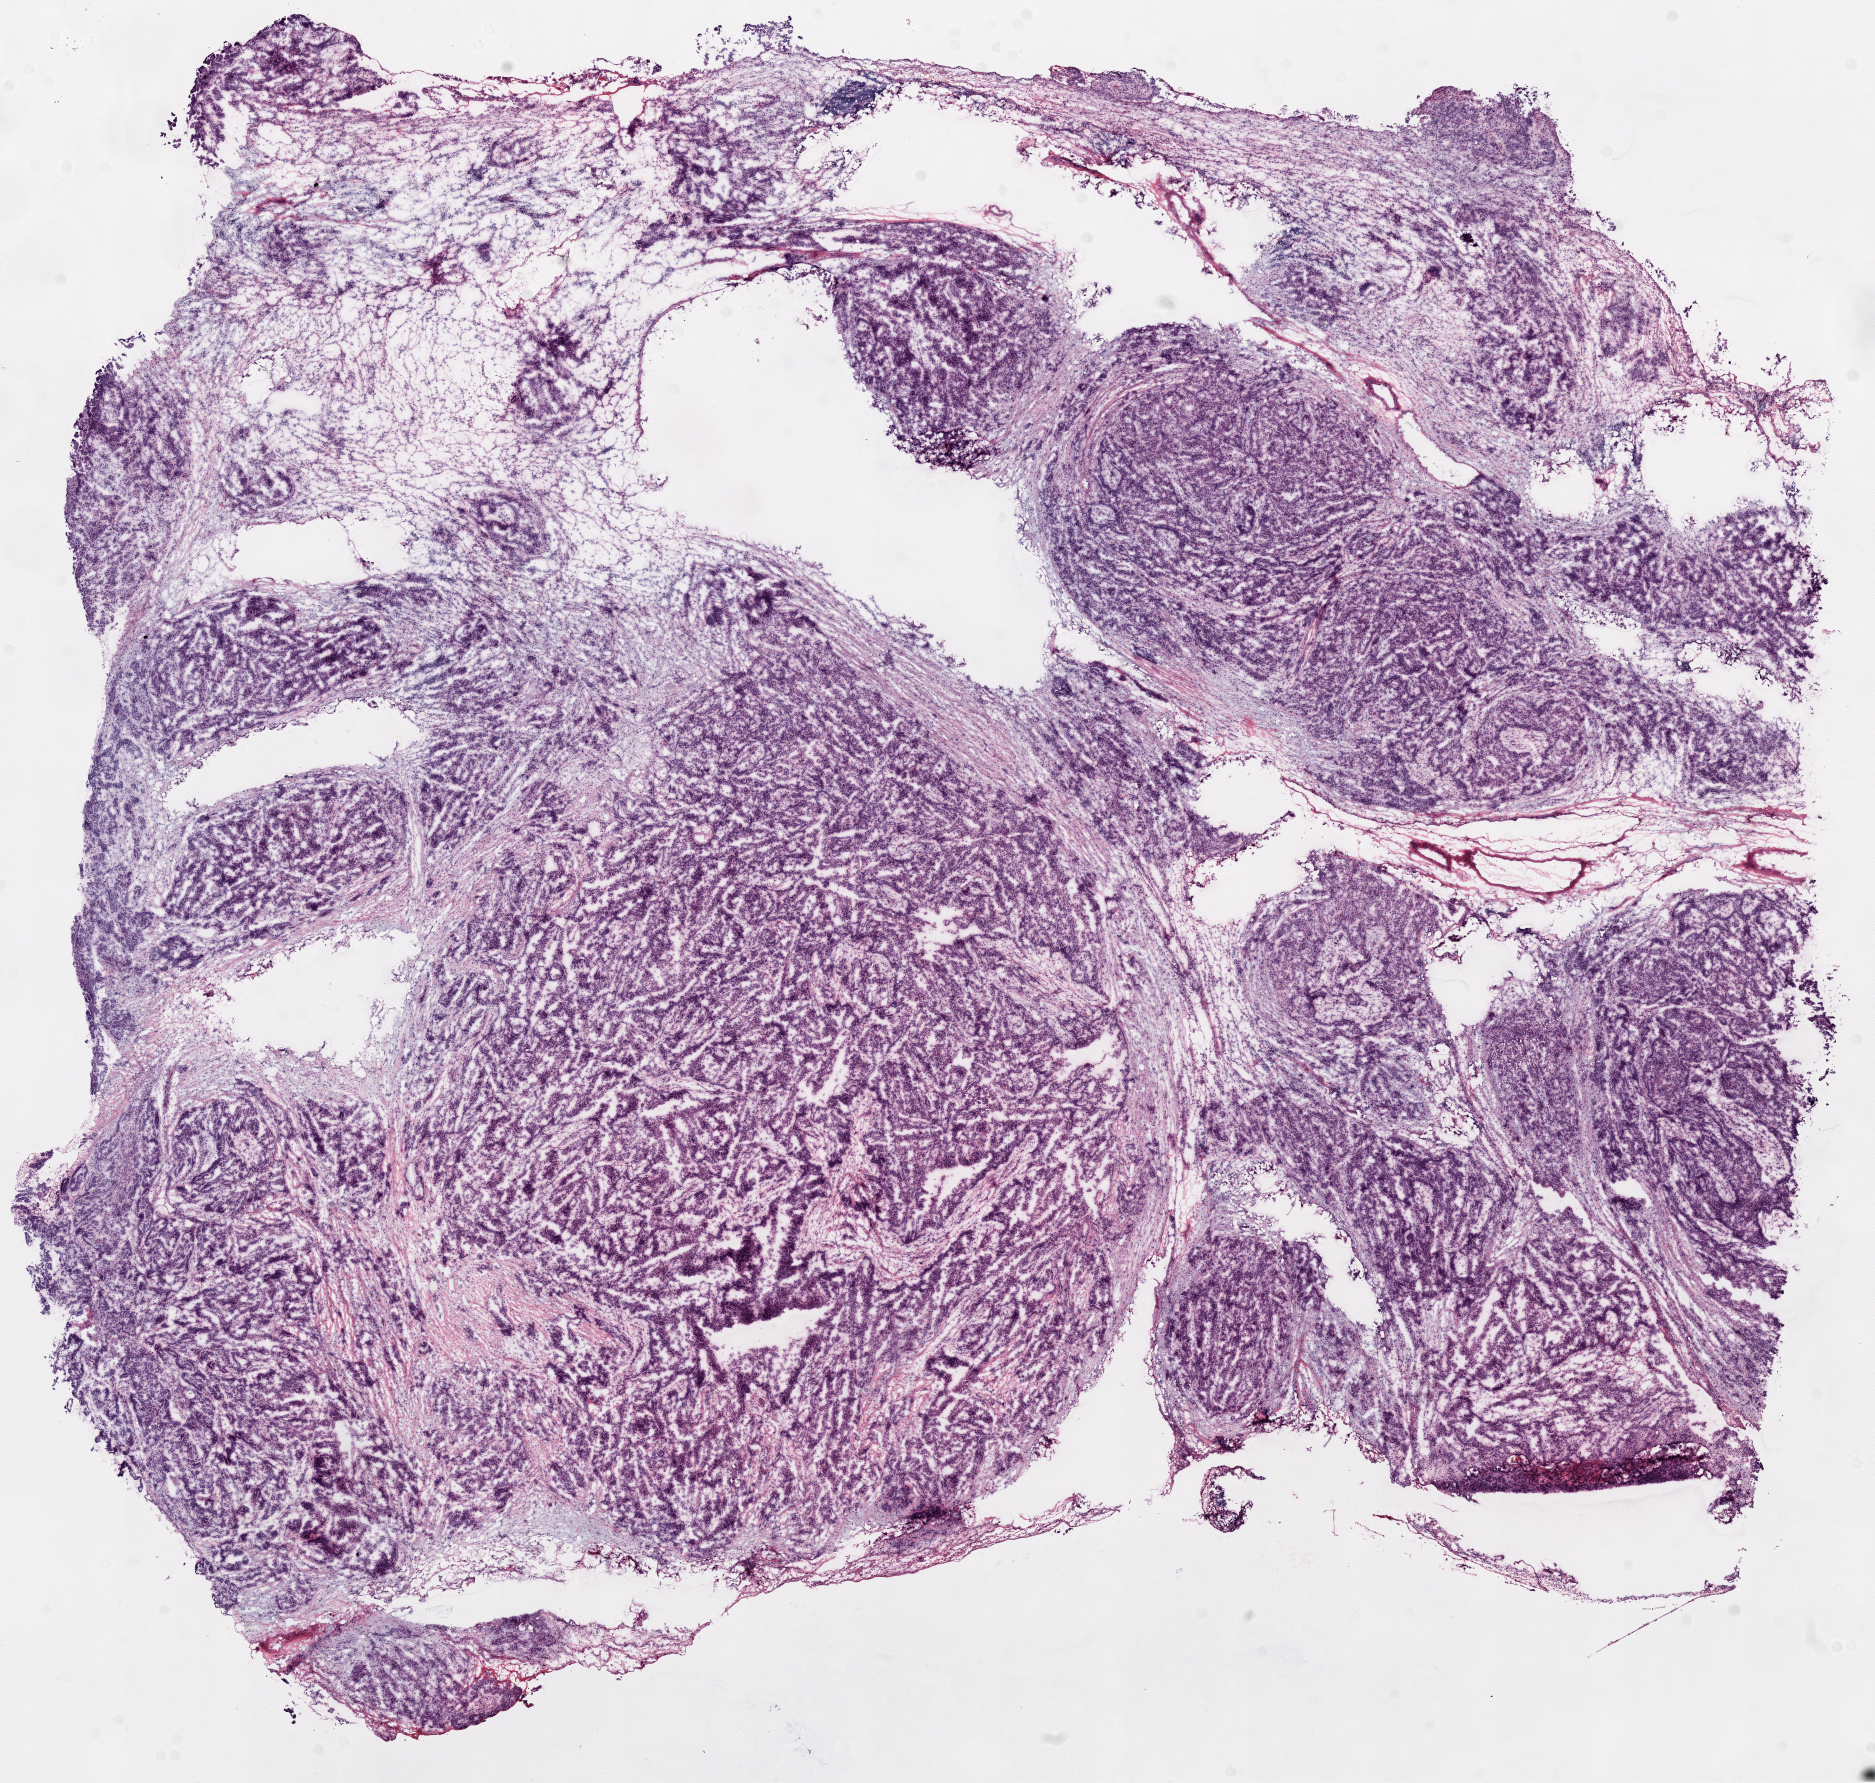
Digitized Hematoxylin and eosin (H&E) stained tissue section (whole slide), low-resolution overview of the scanned area, about 15.0 x 14.3 mm. Frozen section from the top of the tissue portion. Sample: primary tumour, ovary. Female patient; age at initial diagnosis 49 years. Histologic grade: G3 (poorly differentiated). Composition of this section per pathologist review: tumour cells 84%, tumour nuclei 85%, normal cells 0%, stromal cells 15%, necrosis 1%.
- FIGO stage: IV
- diagnosis: Serous cystadenocarcinoma, NOS
- laterality: bilateral